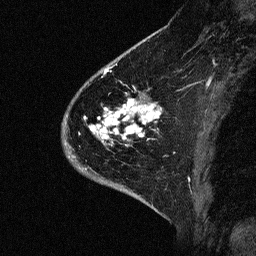
Breast MRI (dynamic contrast-enhanced), one sagittal slice. Slice 17 of 64 in the series (ordered by position). Dynamic contrast-enhanced study with each time point stored as its own series, time point 2 of 3 at this slice position (early post-contrast, ordered by acquisition time). 1.5 T. TE 4.5 ms, TR 11 ms. 2.06 mm slice thickness. 256 × 256 image matrix, field of view 200 × 200 mm. Female patient, age 46 years. Case-level facts recorded for this patient, not image findings: setting: breast cancer imaged before/during neoadjuvant chemotherapy; receptor status: HER2-positive.
Annotated regions visible in this slice (semi-automatically segmented with operator editing):
- analysis volume of interest (the breast-tissue region the enhancement analysis was run in; not a lesion): box from (x=43, y=72) to (x=176, y=177) px
- tumour enhancement mask (voxels above the 90 % enhancement threshold inside the analysis volume of interest): (x=89, y=72)–(x=160, y=141)